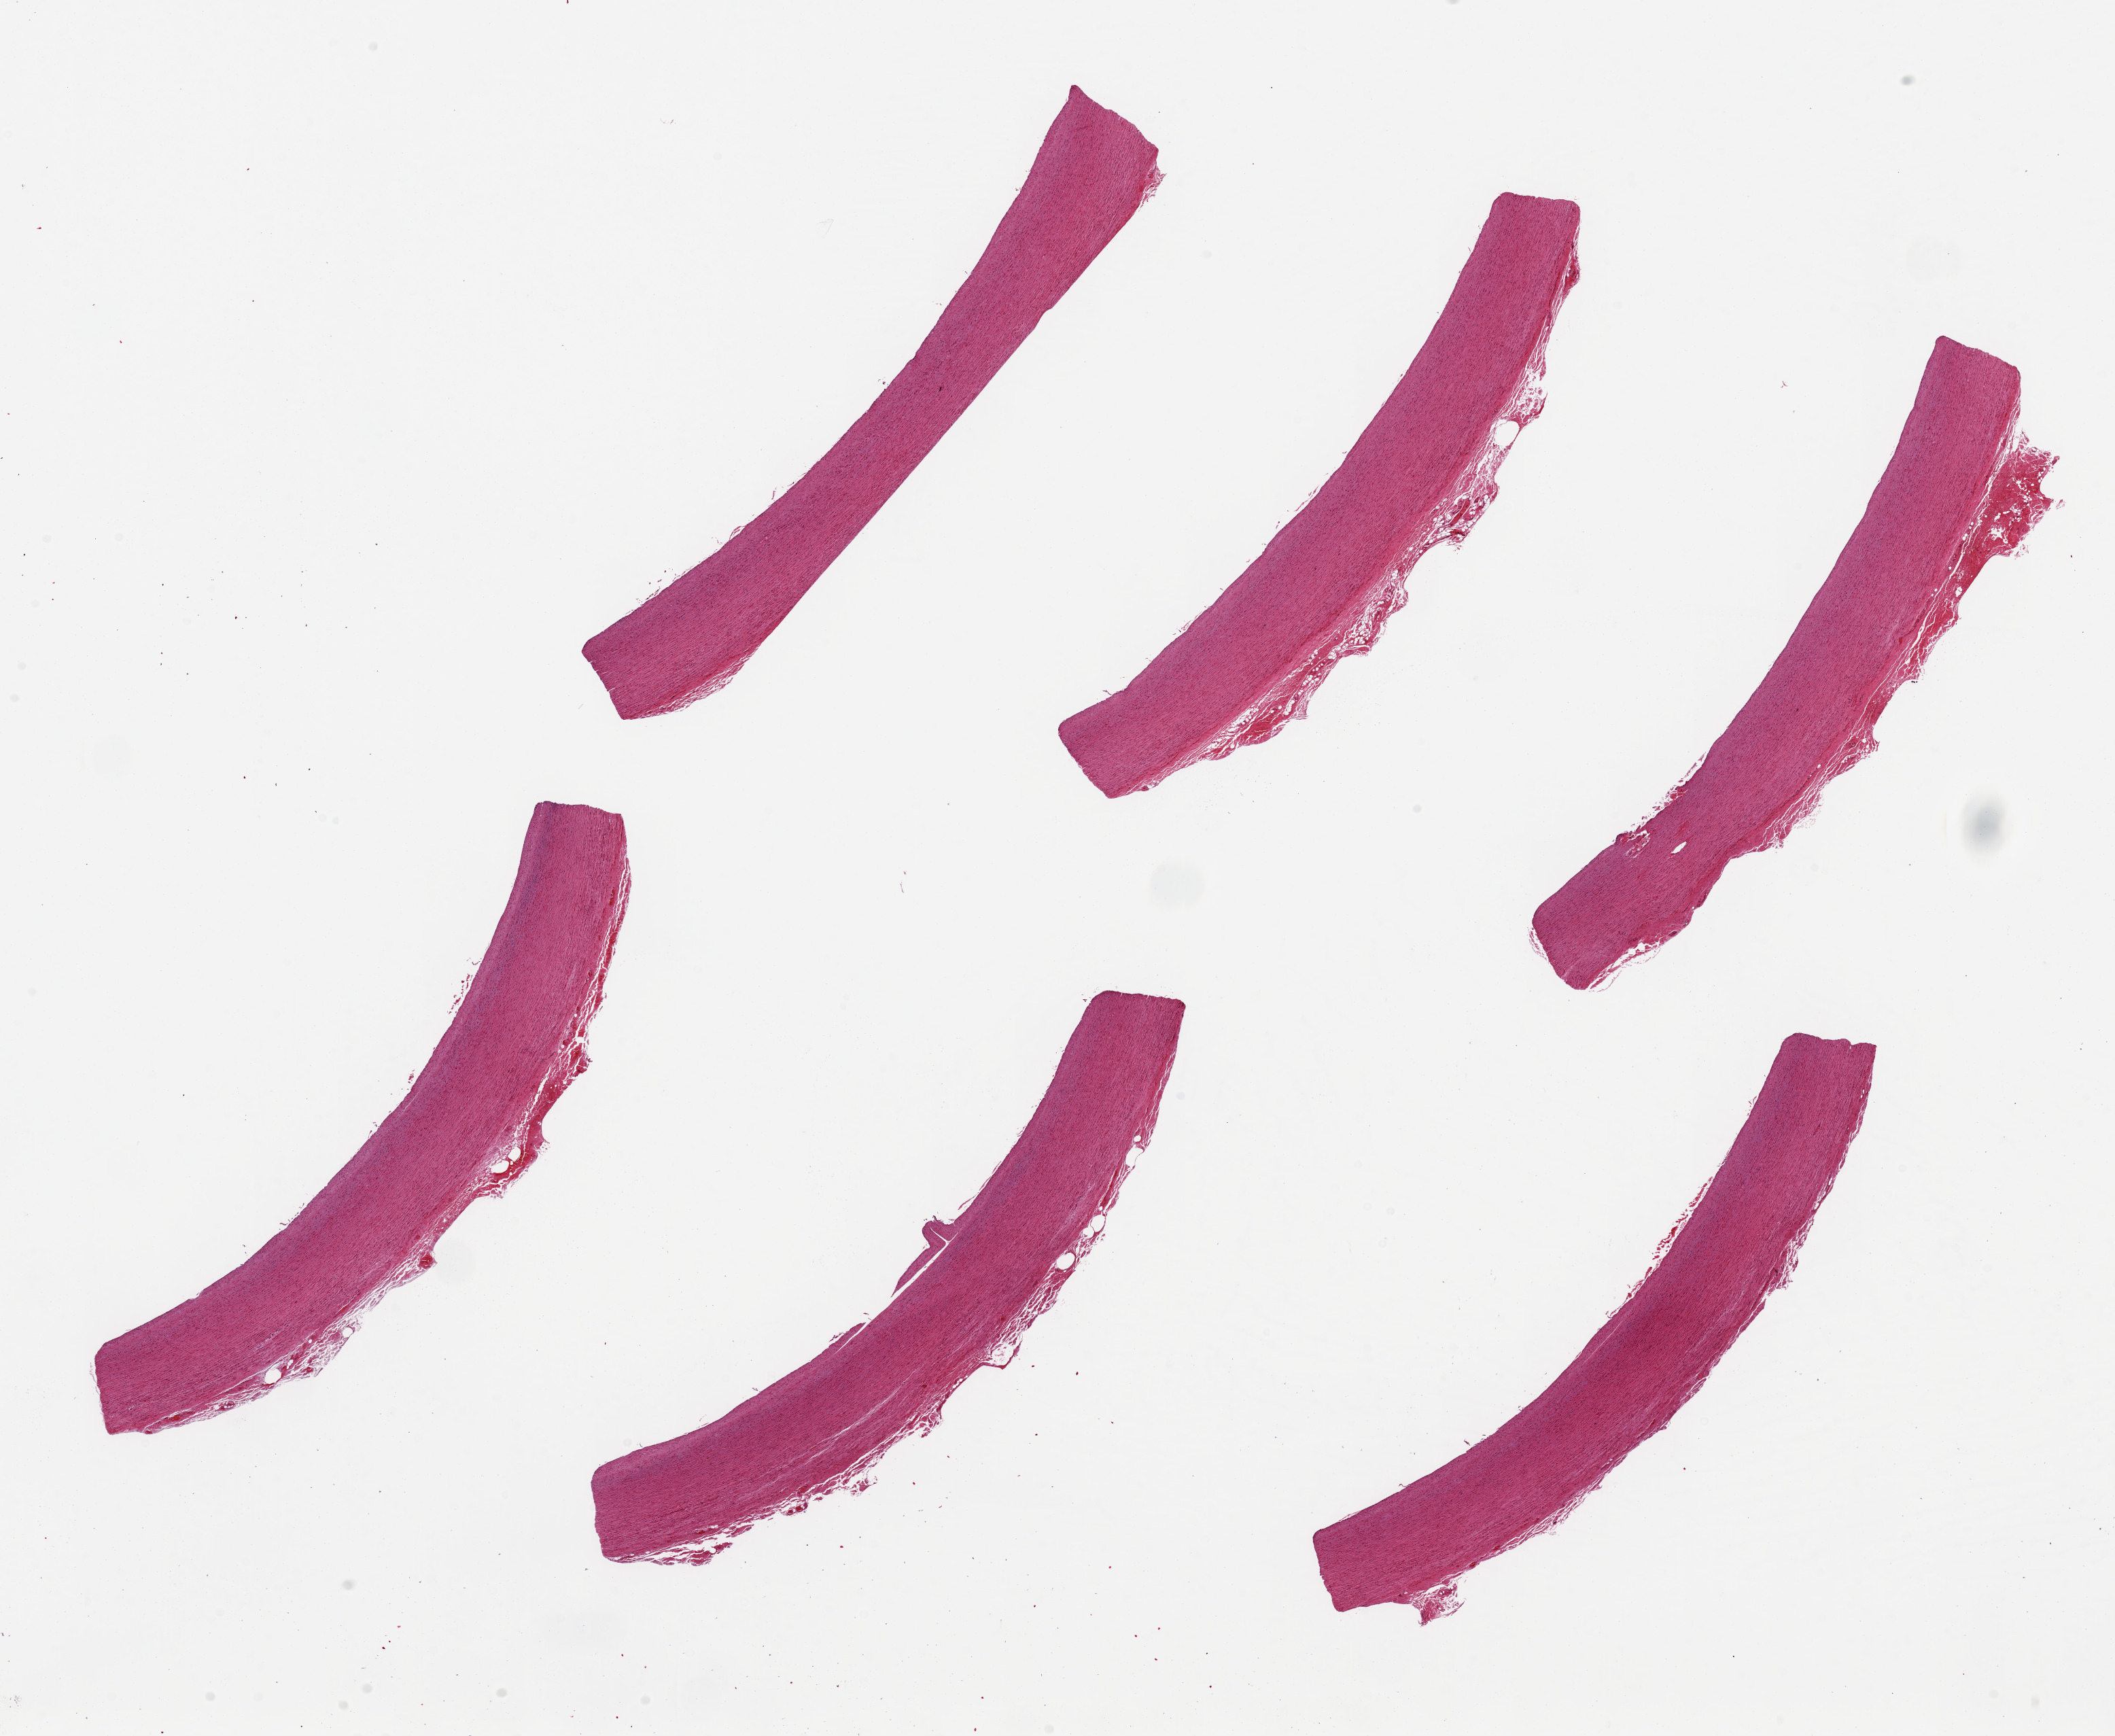
Digitized haematoxylin and eosin-stained section, brightfield, whole scanned area (about 24.6 x 20.2 mm, slide scanned at 20x) shown as a low-resolution overview, PAXgene-fixed paraffin-embedded (PFPE) section, target tissue: aorta, donor tissue sample. Donor: male.
Reviewer comment on this tissue sample: 6 pieces up to 9x1.4 mm.